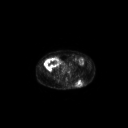
FDG PET of an extremity soft-tissue mass (from a PET/CT study), one axial slice. Slice 93 of 267 in the series (ordered by position). 128 × 128 image matrix, field of view 700 × 700 mm. Male patient, age 69 years. From the clinical record (not read from this slice): histological type: leiomyosarcoma; grade: intermediate; site of the primary tumour: left pelvis.
Structures marked on this image (expert contour drawn on MRI and transferred to this co-registered scan by the dataset authors):
- gross tumour volume (mass): box from (x=76, y=79) to (x=83, y=87) px